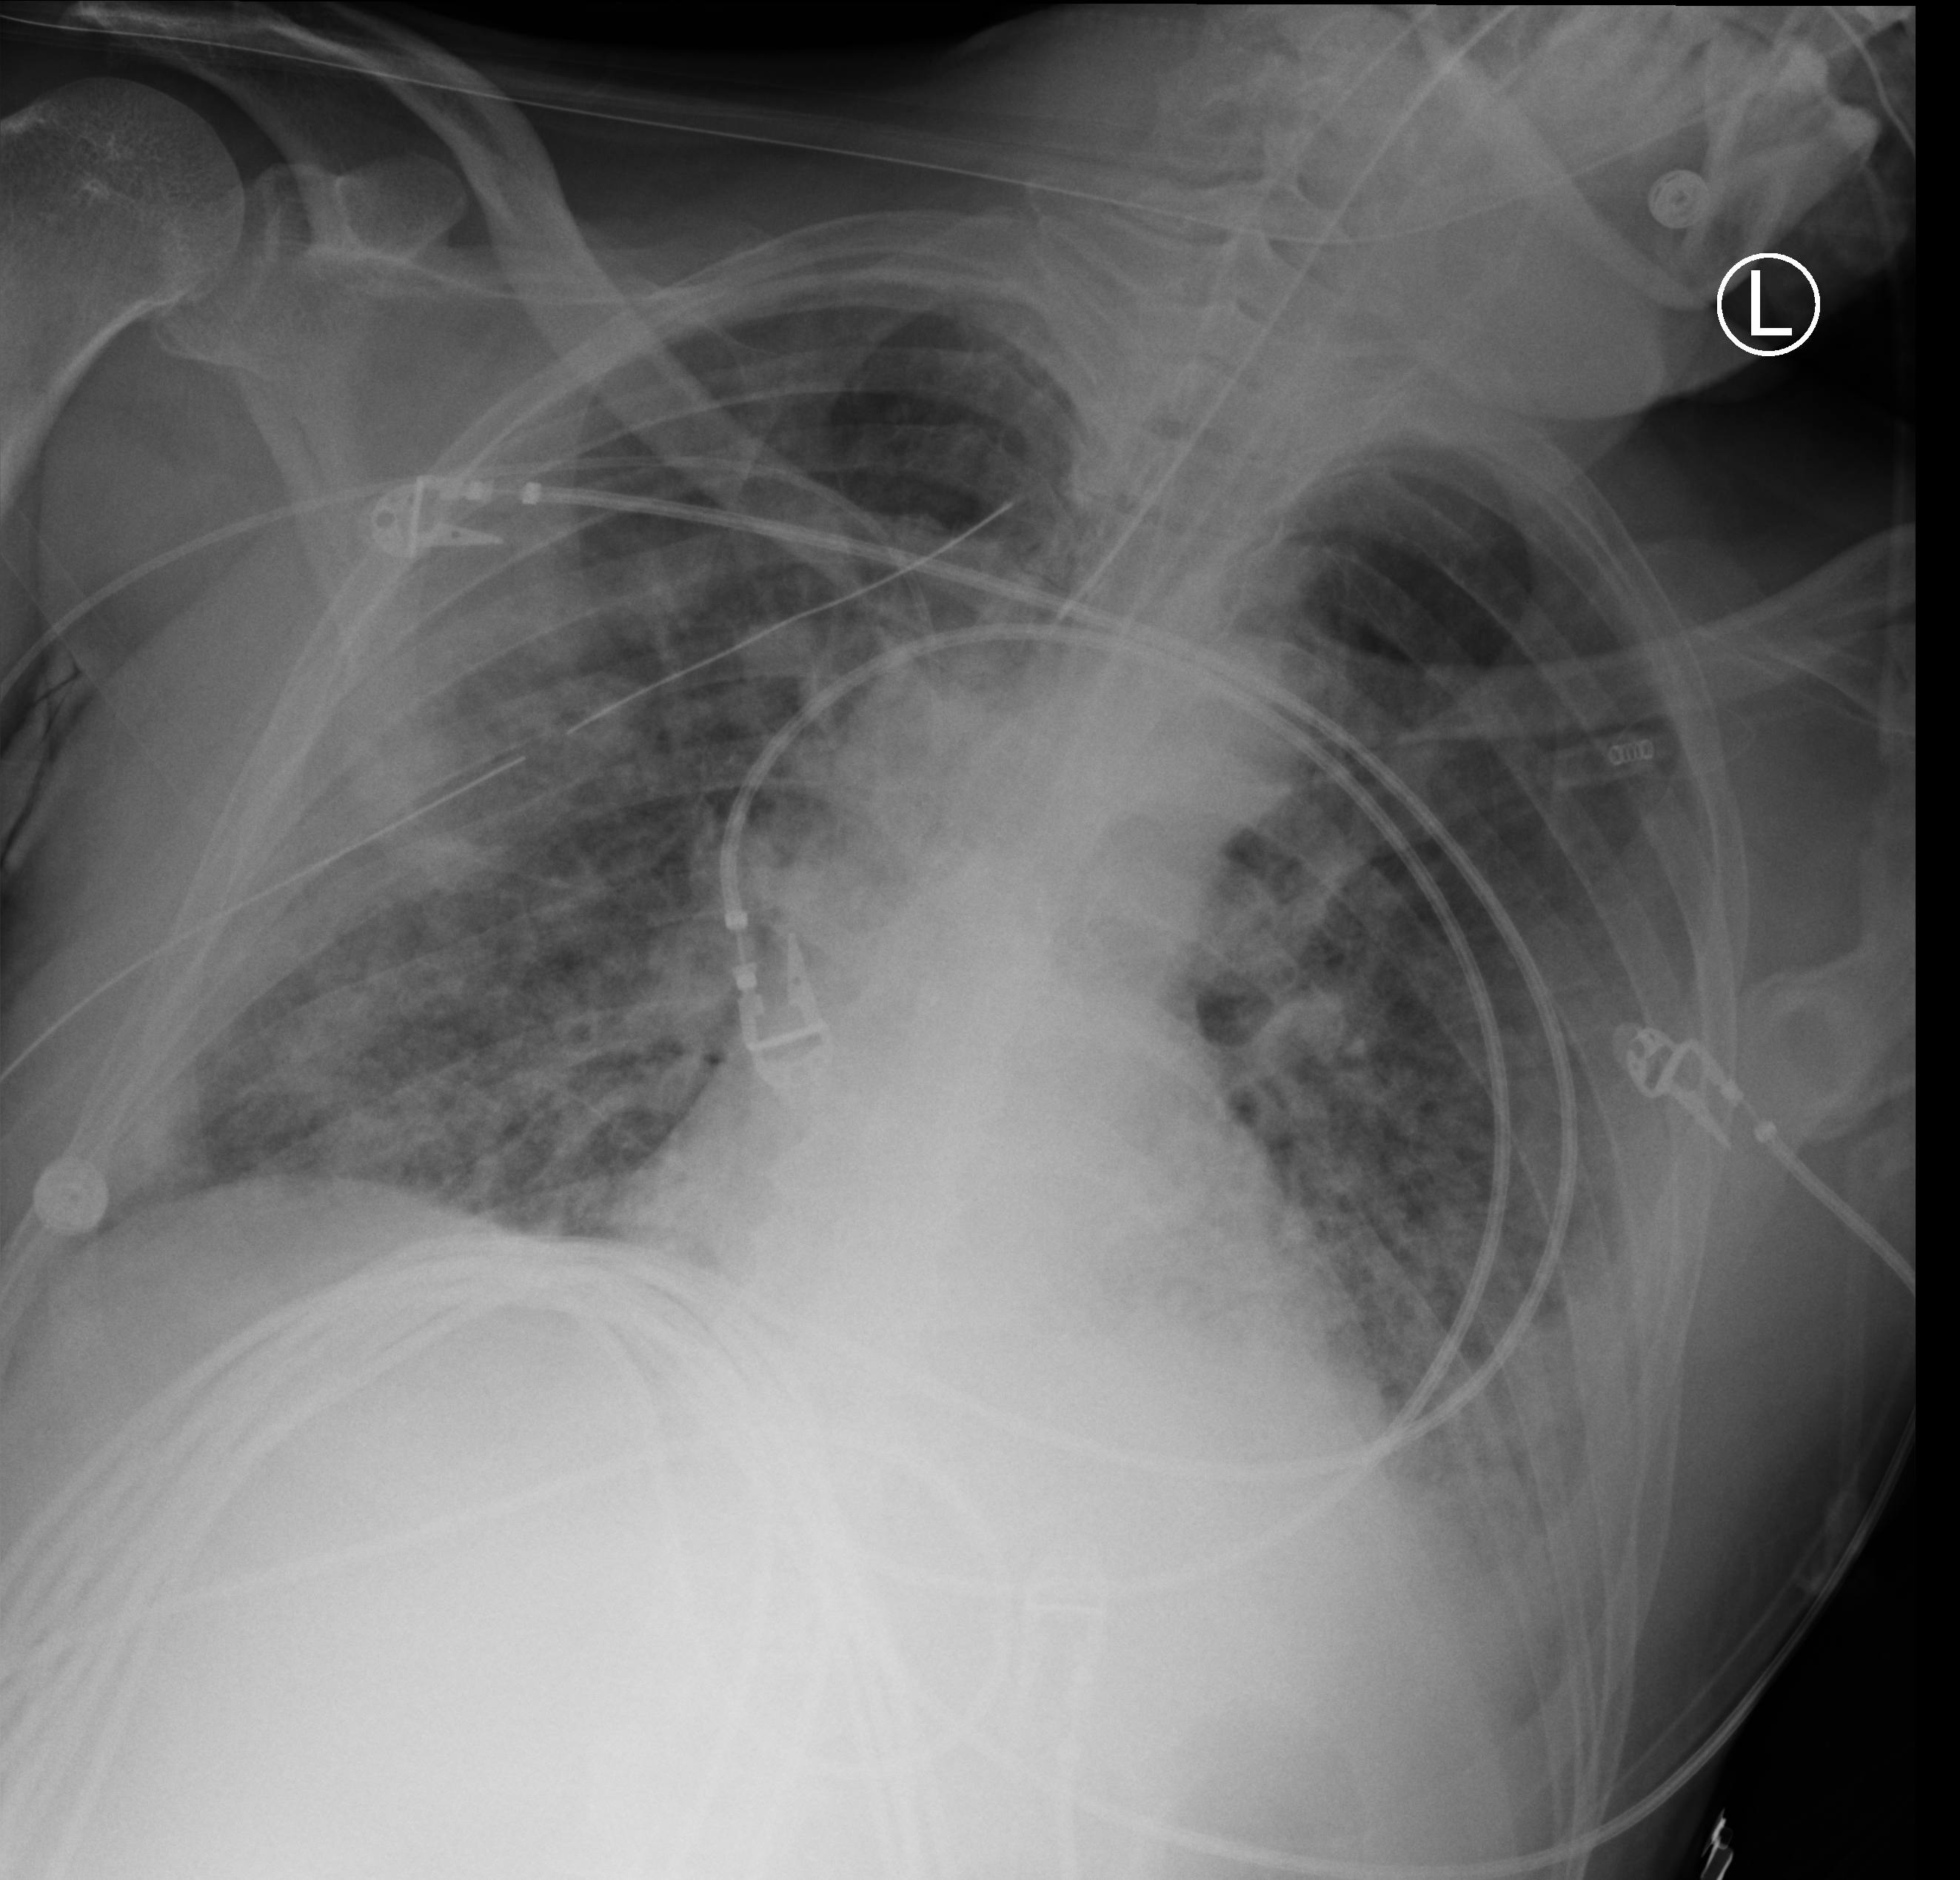
Bedside chest radiograph (computed radiography); anteroposterior (AP) projection. Patient hospitalised with COVID-19; male, aged 18–59 years.
Hospital-stay facts (about this admission, not read from this image; timing relative to this image not recorded):
- hypertension (admission record): no
- COPD (admission record): no
- mechanically ventilated during this hospital stay: yes